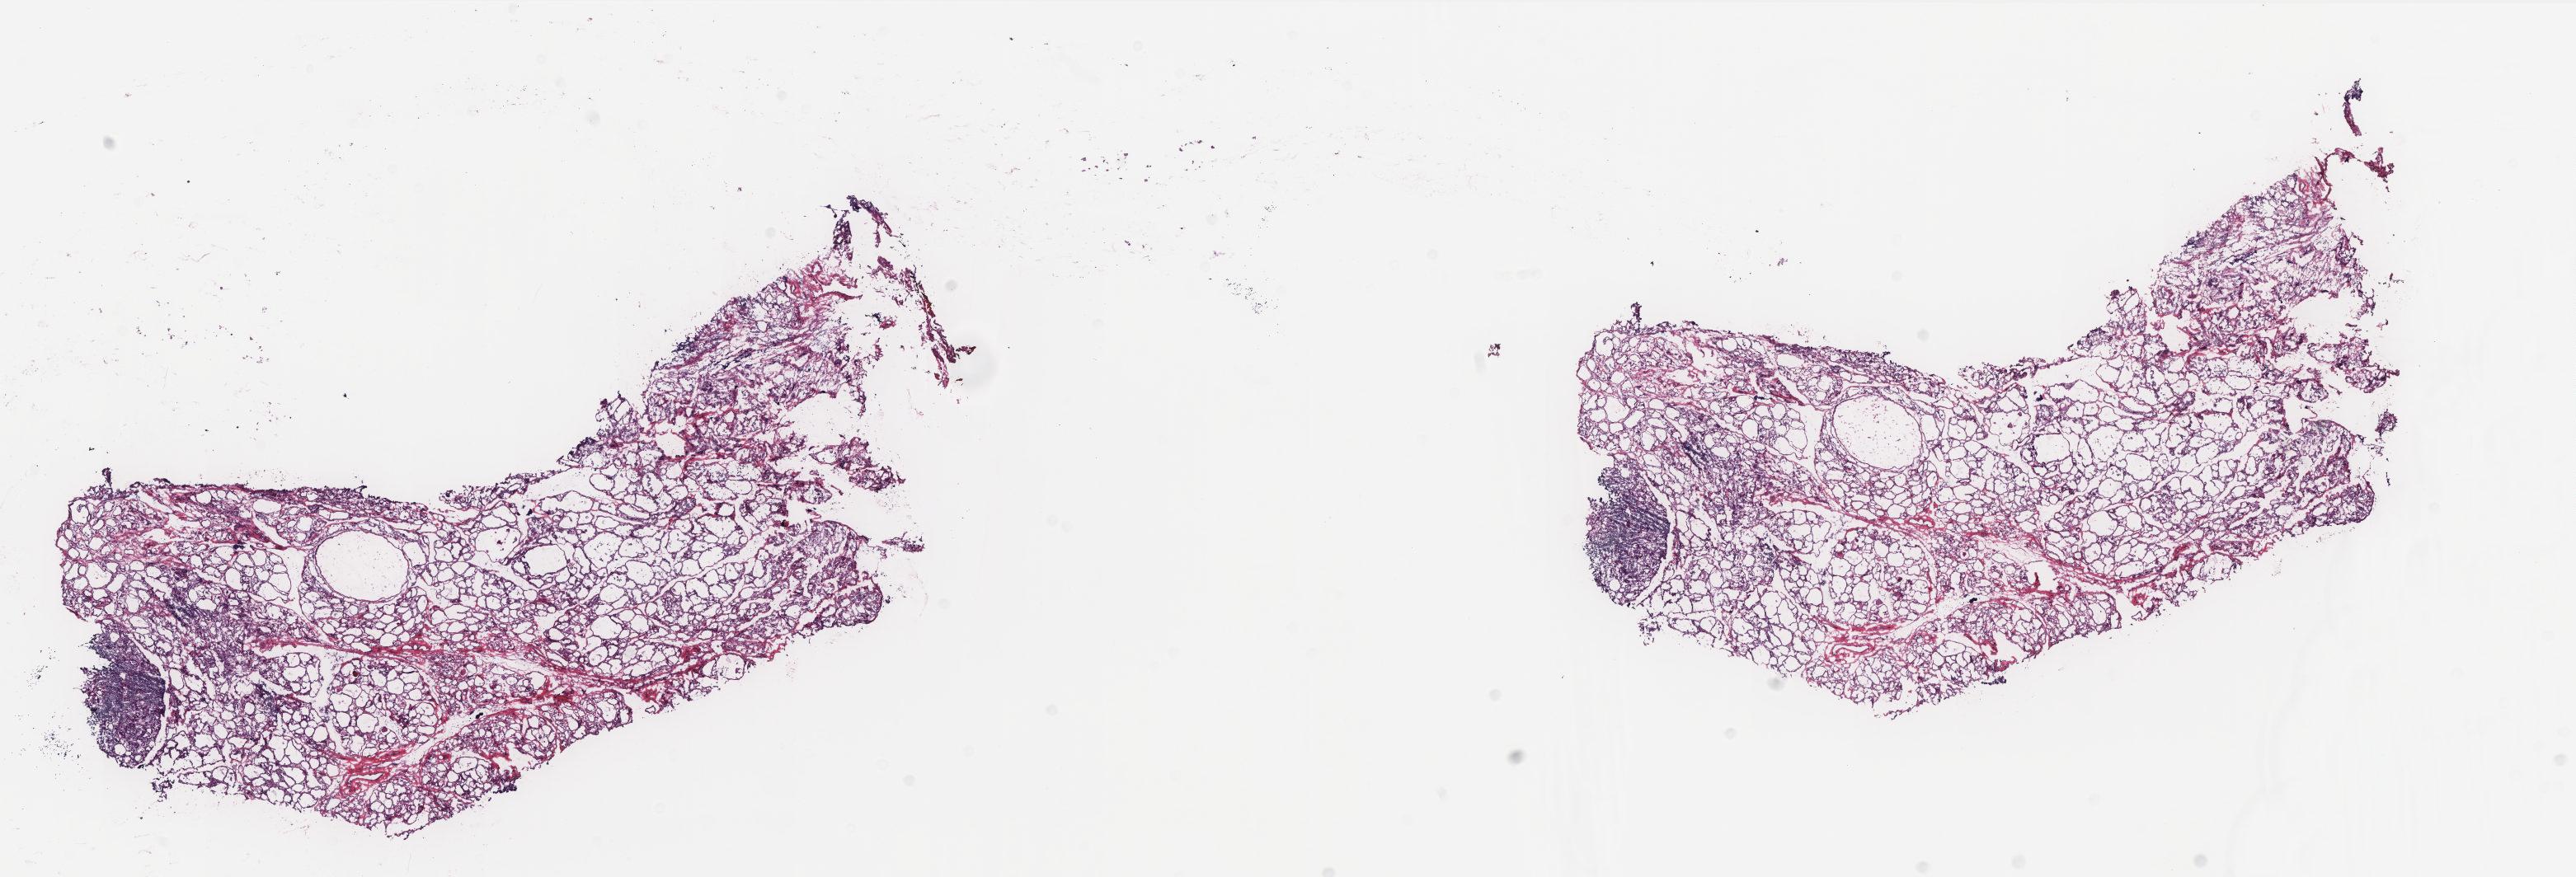
Whole-slide histology image, H&E — whole scanned area (about 25.0 x 8.5 mm, slide scanned at 20x) shown as a low-resolution overview; frozen section from the top of the tissue portion; thyroid, solid tissue normal (non-tumour tissue) sample. Patient: female, age at initial diagnosis 42 years. Slide review estimates, as recorded: tumour cells 0%, tumour nuclei 0%, normal cells 60%, stromal cells 40%, necrosis 0%. Infiltration values recorded for this section: lymphocyte infiltration 5%, monocyte infiltration 0%, neutrophil infiltration 0%.
• this section: solid tissue normal sample (biorepository sample class)
• patient diagnosis: Papillary adenocarcinoma, NOS (thyroid gland)